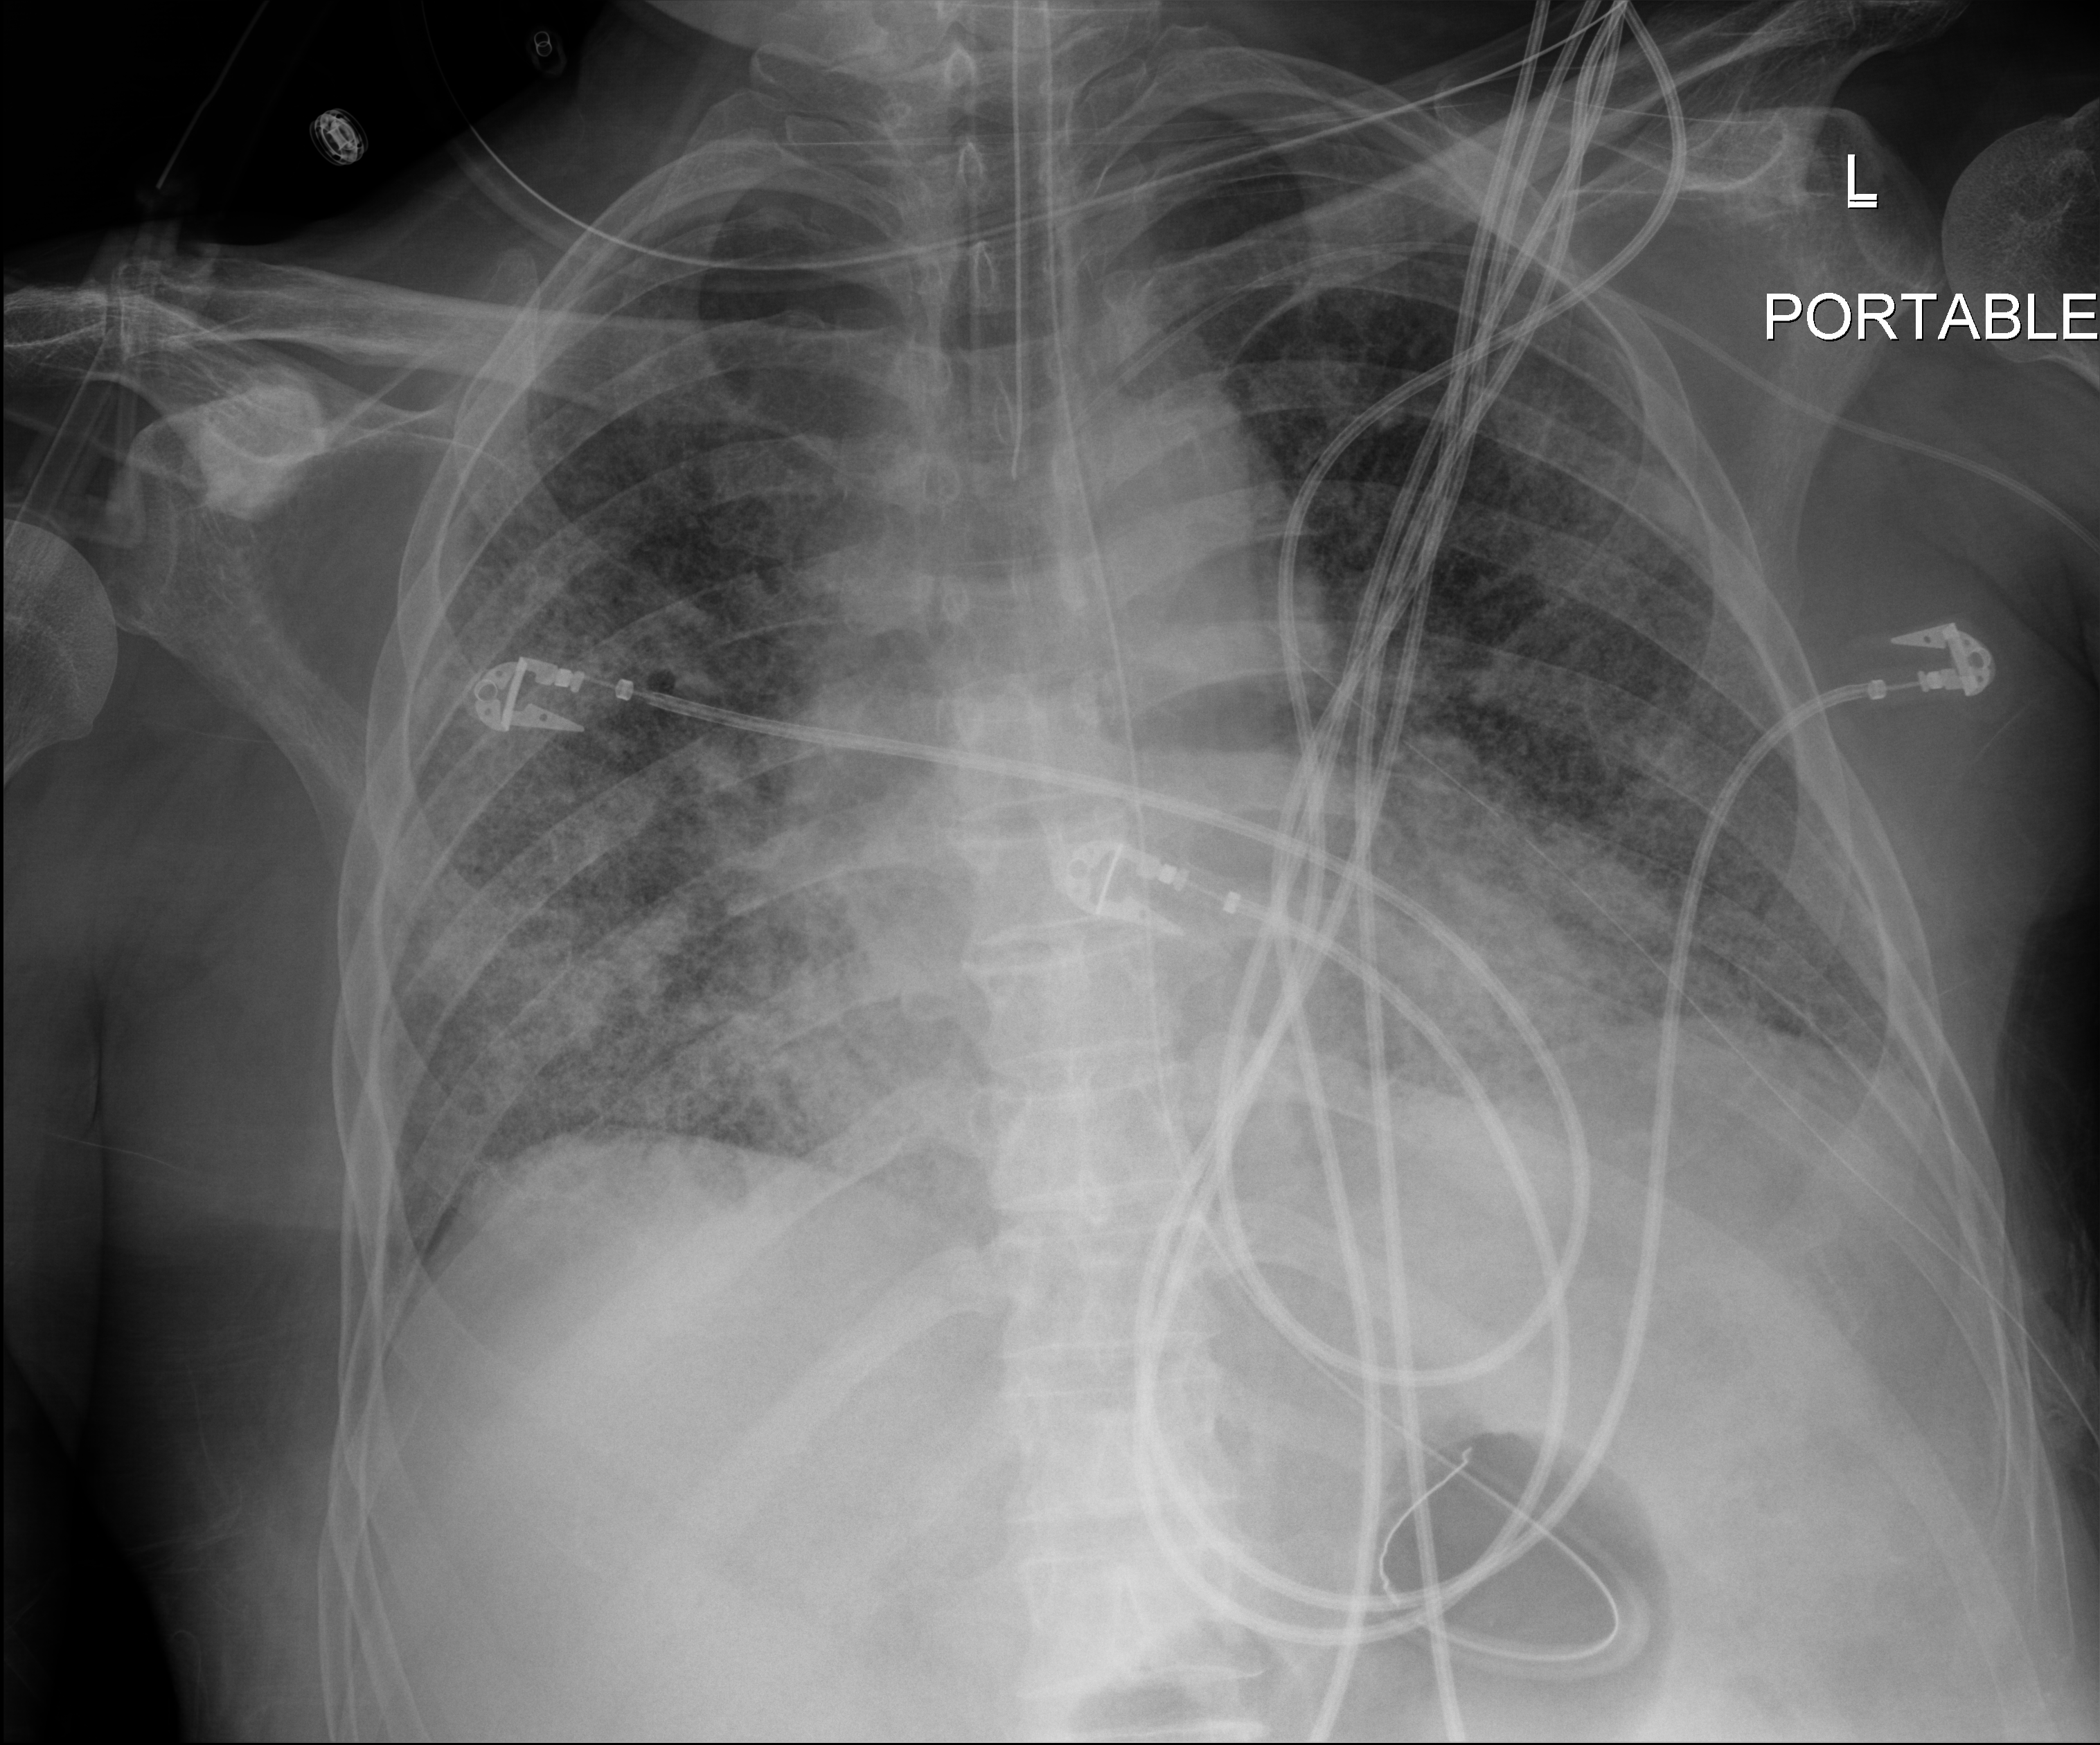
Chest X-ray (portable), anteroposterior (AP) projection. Male patient hospitalised with COVID-19, age 60–74 years.
From the hospital-stay record, not from the radiograph (when in the stay this image was taken is not recorded): admitted to intensive care during this hospital stay: yes; length of hospital stay: 54 days.